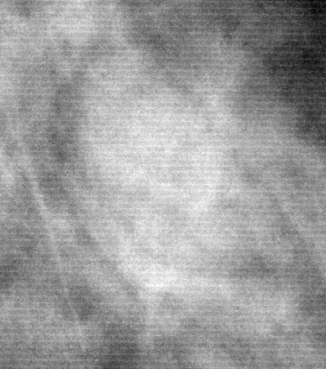
Region of interest cut from a scanned film mammogram (one marked finding); right breast; CC view.
- Marked abnormality: mass, shape oval, margins ill defined; BI-RADS assessment category 4; pathology result (as recorded, not read from the image): benign.